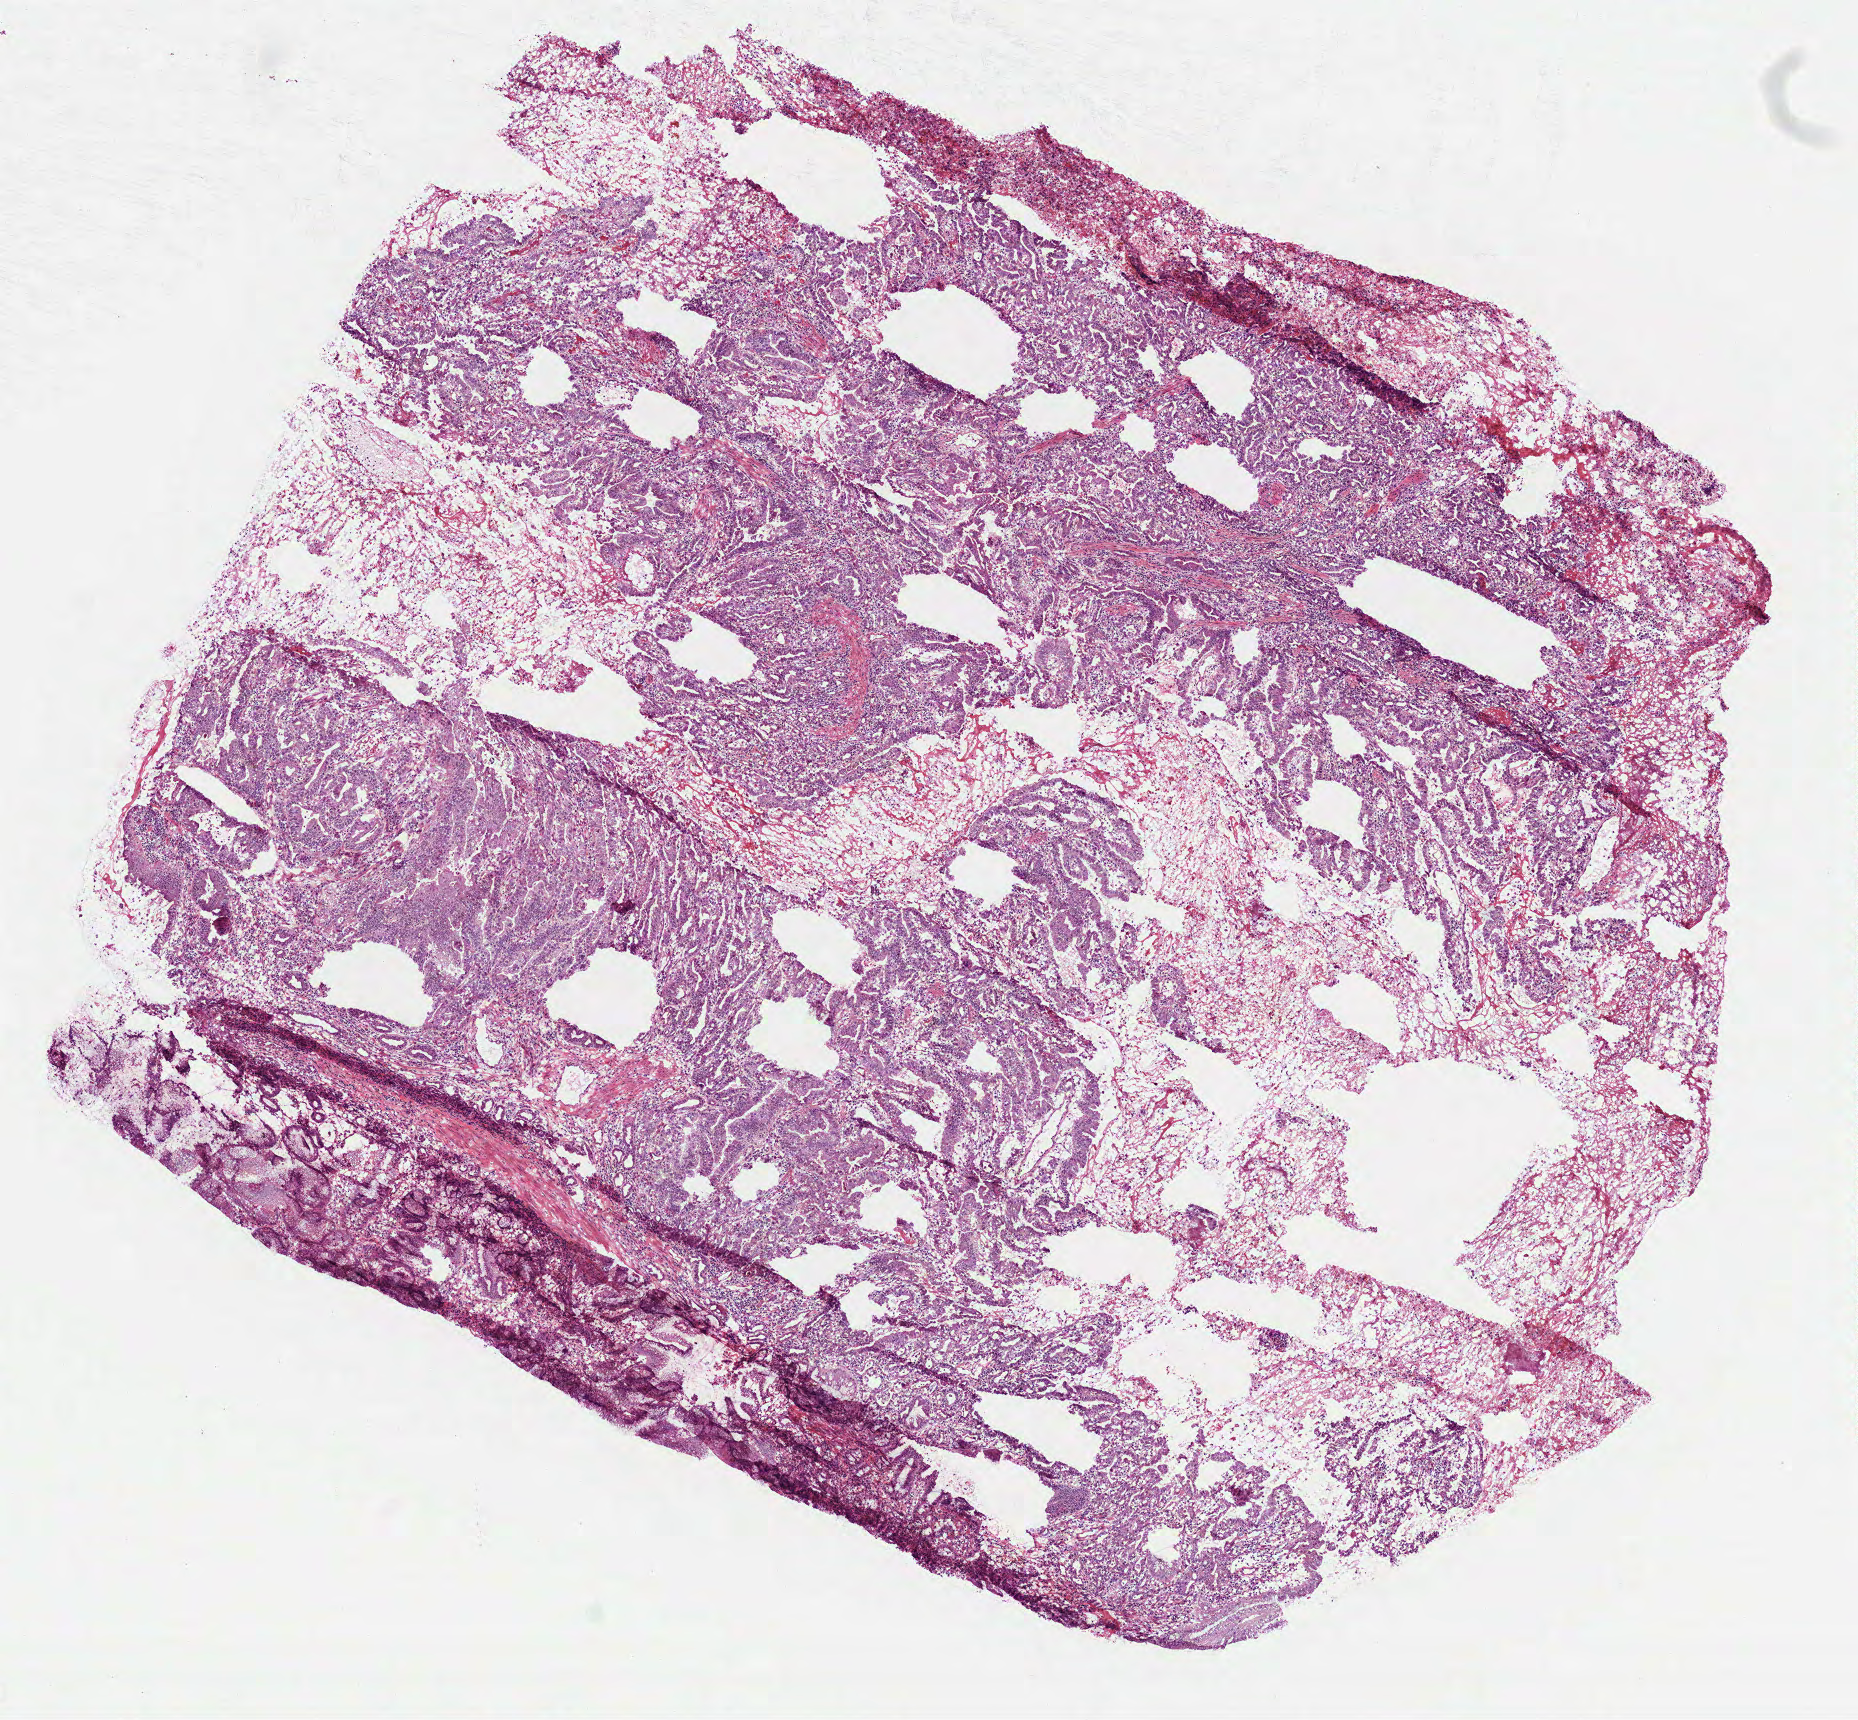
H&E whole-slide image, shown as a low-resolution overview of the whole scanned area (about 7.5 x 6.9 mm, from a 40x scan); frozen section from the top of the tissue portion; stomach, primary tumour sample. Patient sex: female. Histologic grade: G2 (moderately differentiated). Pathologist review of this section (percent, as recorded): tumour cells 70%, tumour nuclei 70%, normal cells 5%, stromal cells 20%, necrosis 5%.
Diagnosis: Adenocarcinoma, NOS. AJCC pathologic stage: IB.